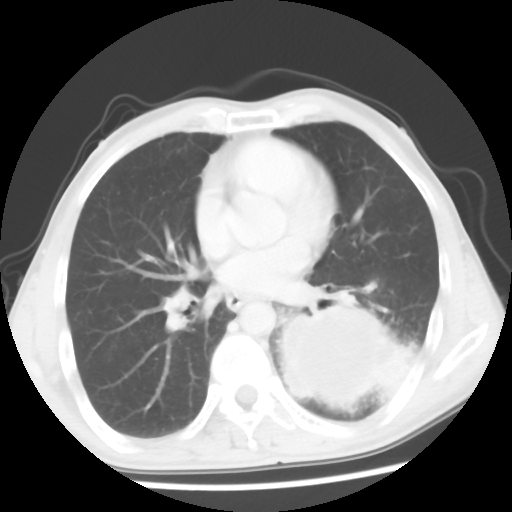
Chest CT, one axial slice. Position 27 of 56 along the scan axis. 120 kVp. Lung window (W 1500 / L -600 HU). 5 mm slice thickness. 512 × 512 image matrix, field of view 318 × 318 mm. Patient: male, 60 years. From the clinical record (not read from this slice): clinical TNM (as recorded): T4 N0 M0.
Annotated regions visible in this slice (bounding box drawn by a radiologist):
- lung tumour (recorded histology: squamous cell carcinoma): box from (x=263, y=286) to (x=439, y=445) px